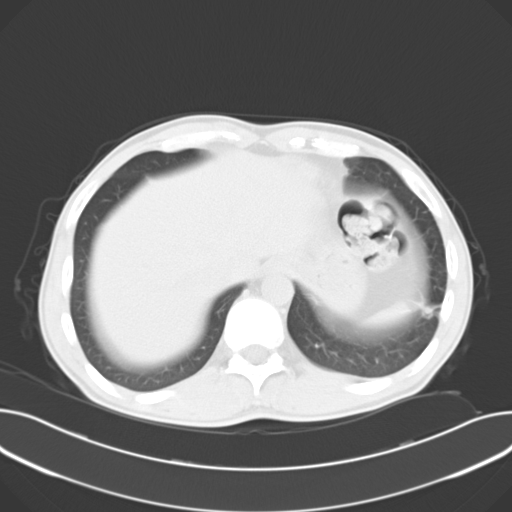
Chest CT, one axial slice. Position 7 of 30 along the scan axis. Reconstruction kernel B40f. Lung window (W 1500 / L -600 HU). 10 mm slice thickness. 512 × 512 image matrix. Male patient, age 44 years. Case-level facts recorded for this patient, not image findings: clinical TNM (as recorded): T1c N0 M1b.
Structures marked on this image (bounding box drawn by a radiologist):
- lung tumour (recorded histology: adenocarcinoma): bounding box [x1, y1, x2, y2] px = [420, 296, 443, 326]